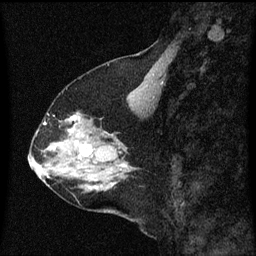
Breast MRI (dynamic contrast-enhanced), one sagittal slice; slice 23 of 60 in the series (ordered by position); dynamic contrast-enhanced series, image 2 of 3 at this slice position (ordered by acquisition); 1.5 T; TE 4.2 ms, TR 8 ms; 256 × 256 image matrix, field of view 200 × 200 mm. Patient: female, 58 years.
Structures marked on this image (semi-automatically segmented with operator editing):
- analysis volume of interest (the breast-tissue region the enhancement analysis was run in; not a lesion): bounding box (x1, y1, x2, y2) in pixels: (56, 118, 99, 149)
- tumour enhancement mask (voxels above the 70 % enhancement threshold inside the analysis volume of interest): (70, 118, 81, 145)